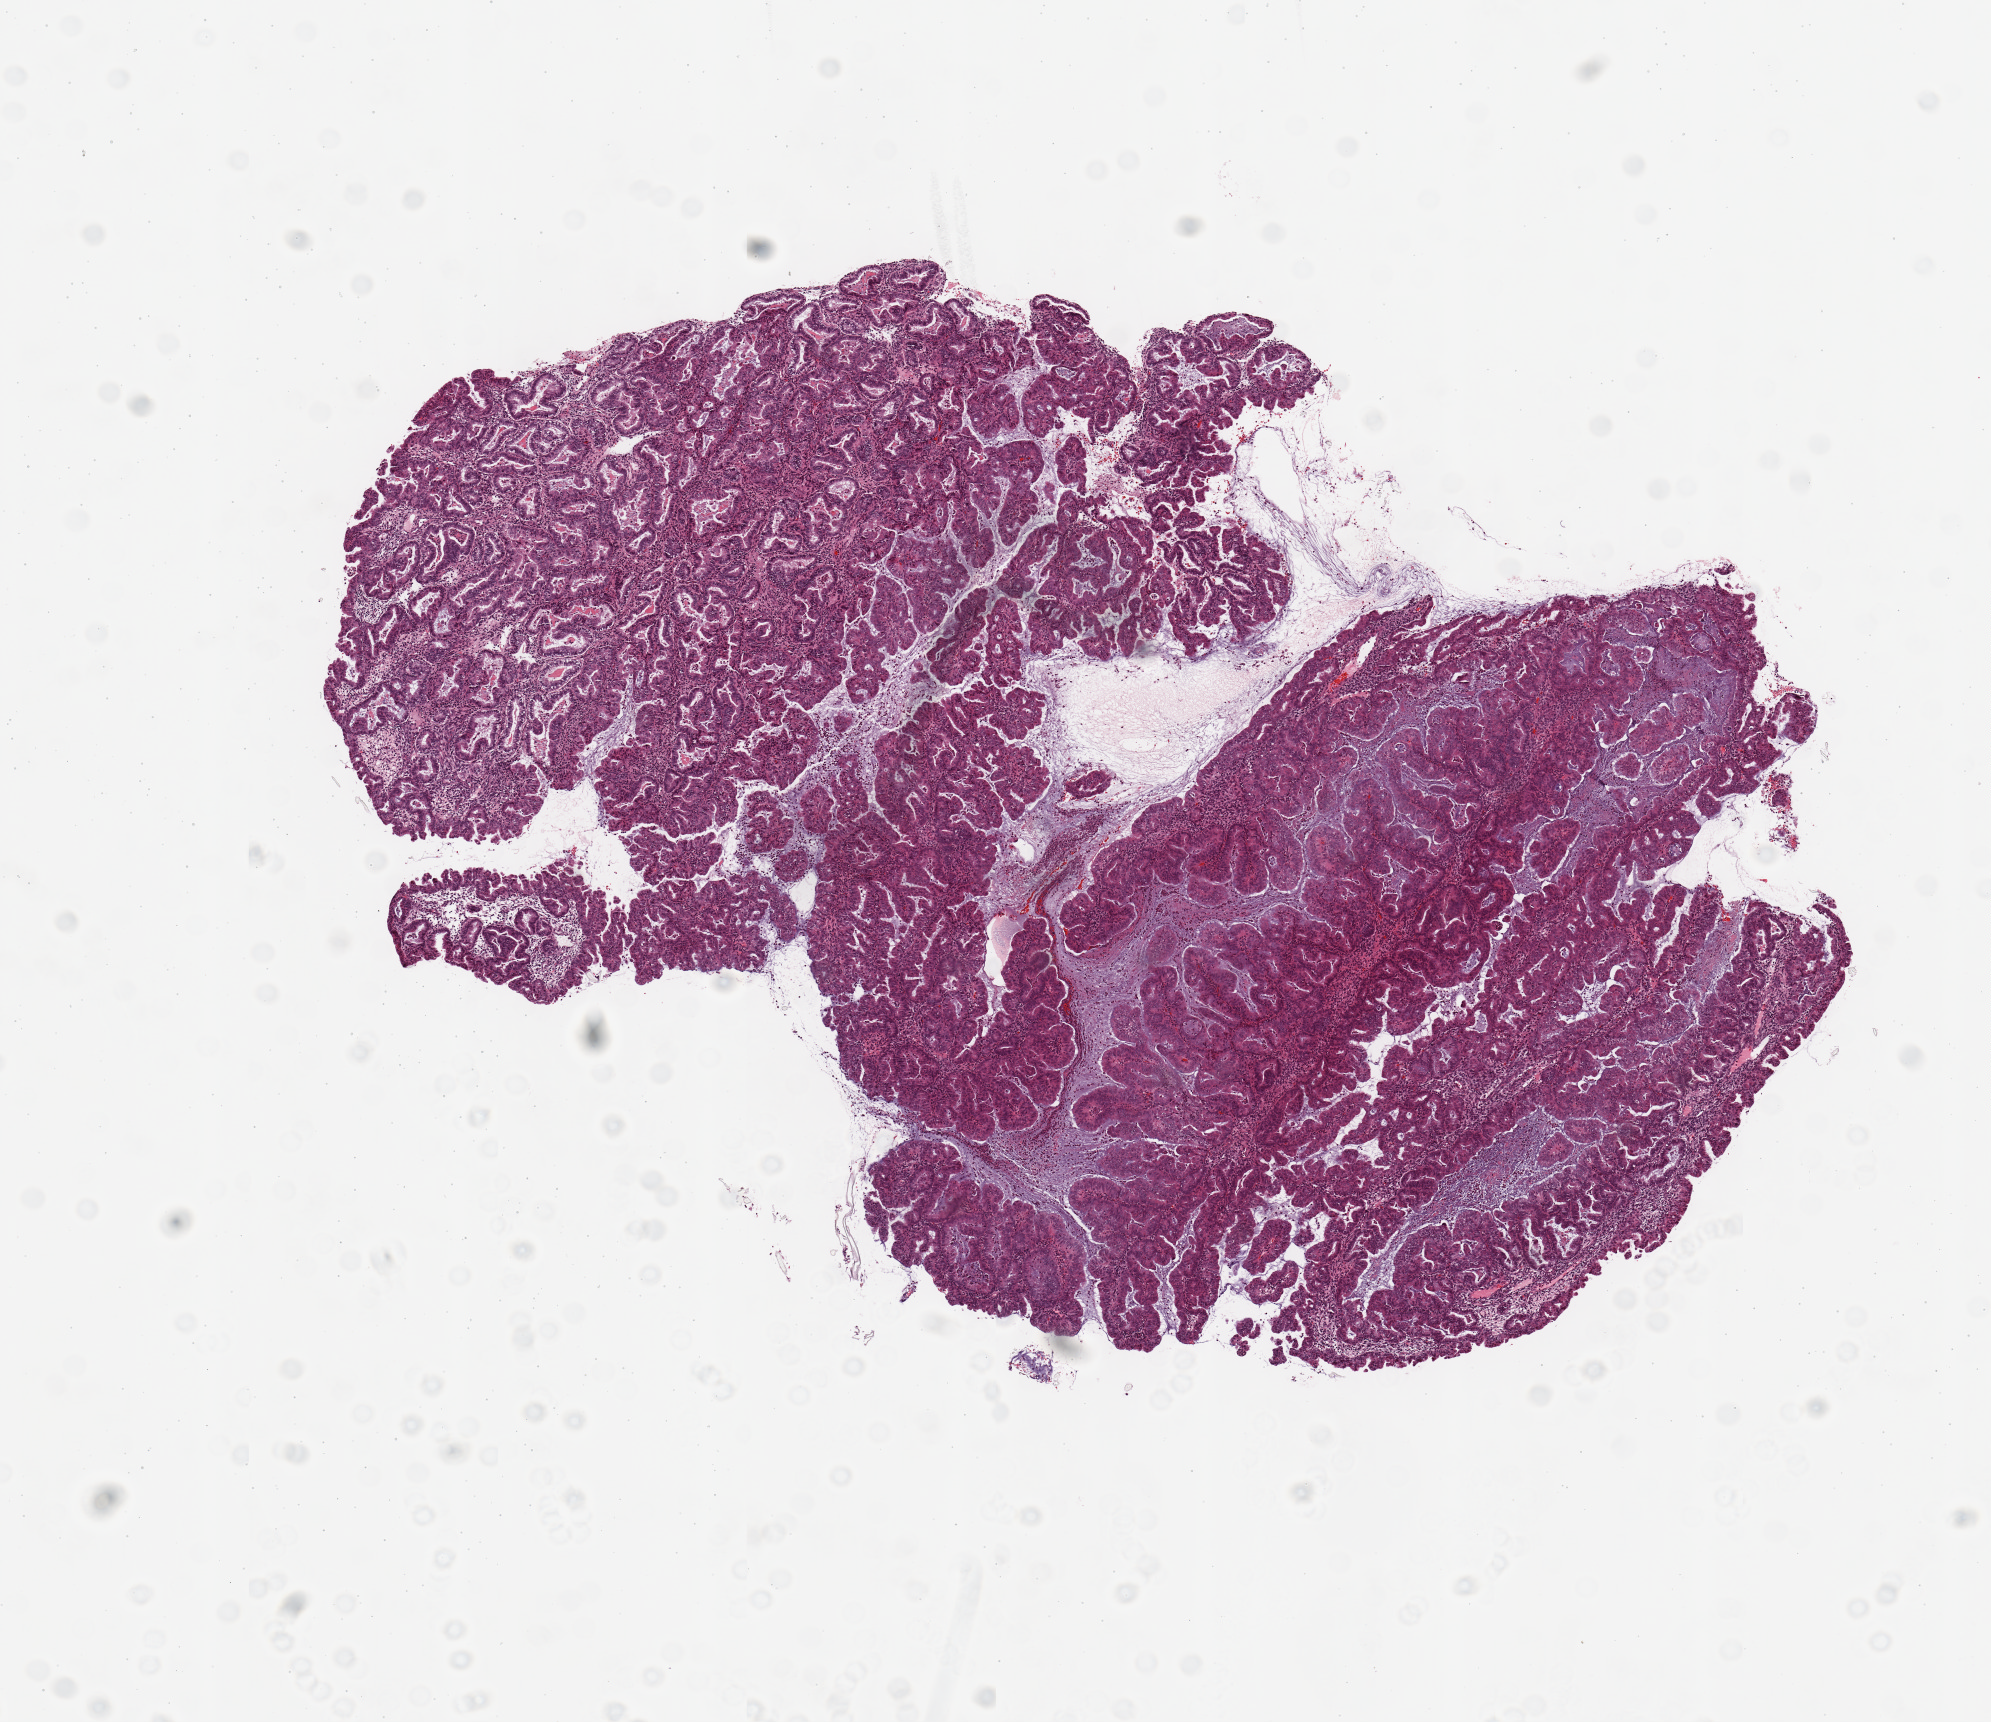
Whole-slide histology image, H&E, a low-resolution overview of the entire scanned area, about 7.9 x 6.8 mm. Uterus, tumour tissue. Female, 49 y/o.
Patient diagnosis (cohort enrolment): corpus endometrial carcinoma (uterus).